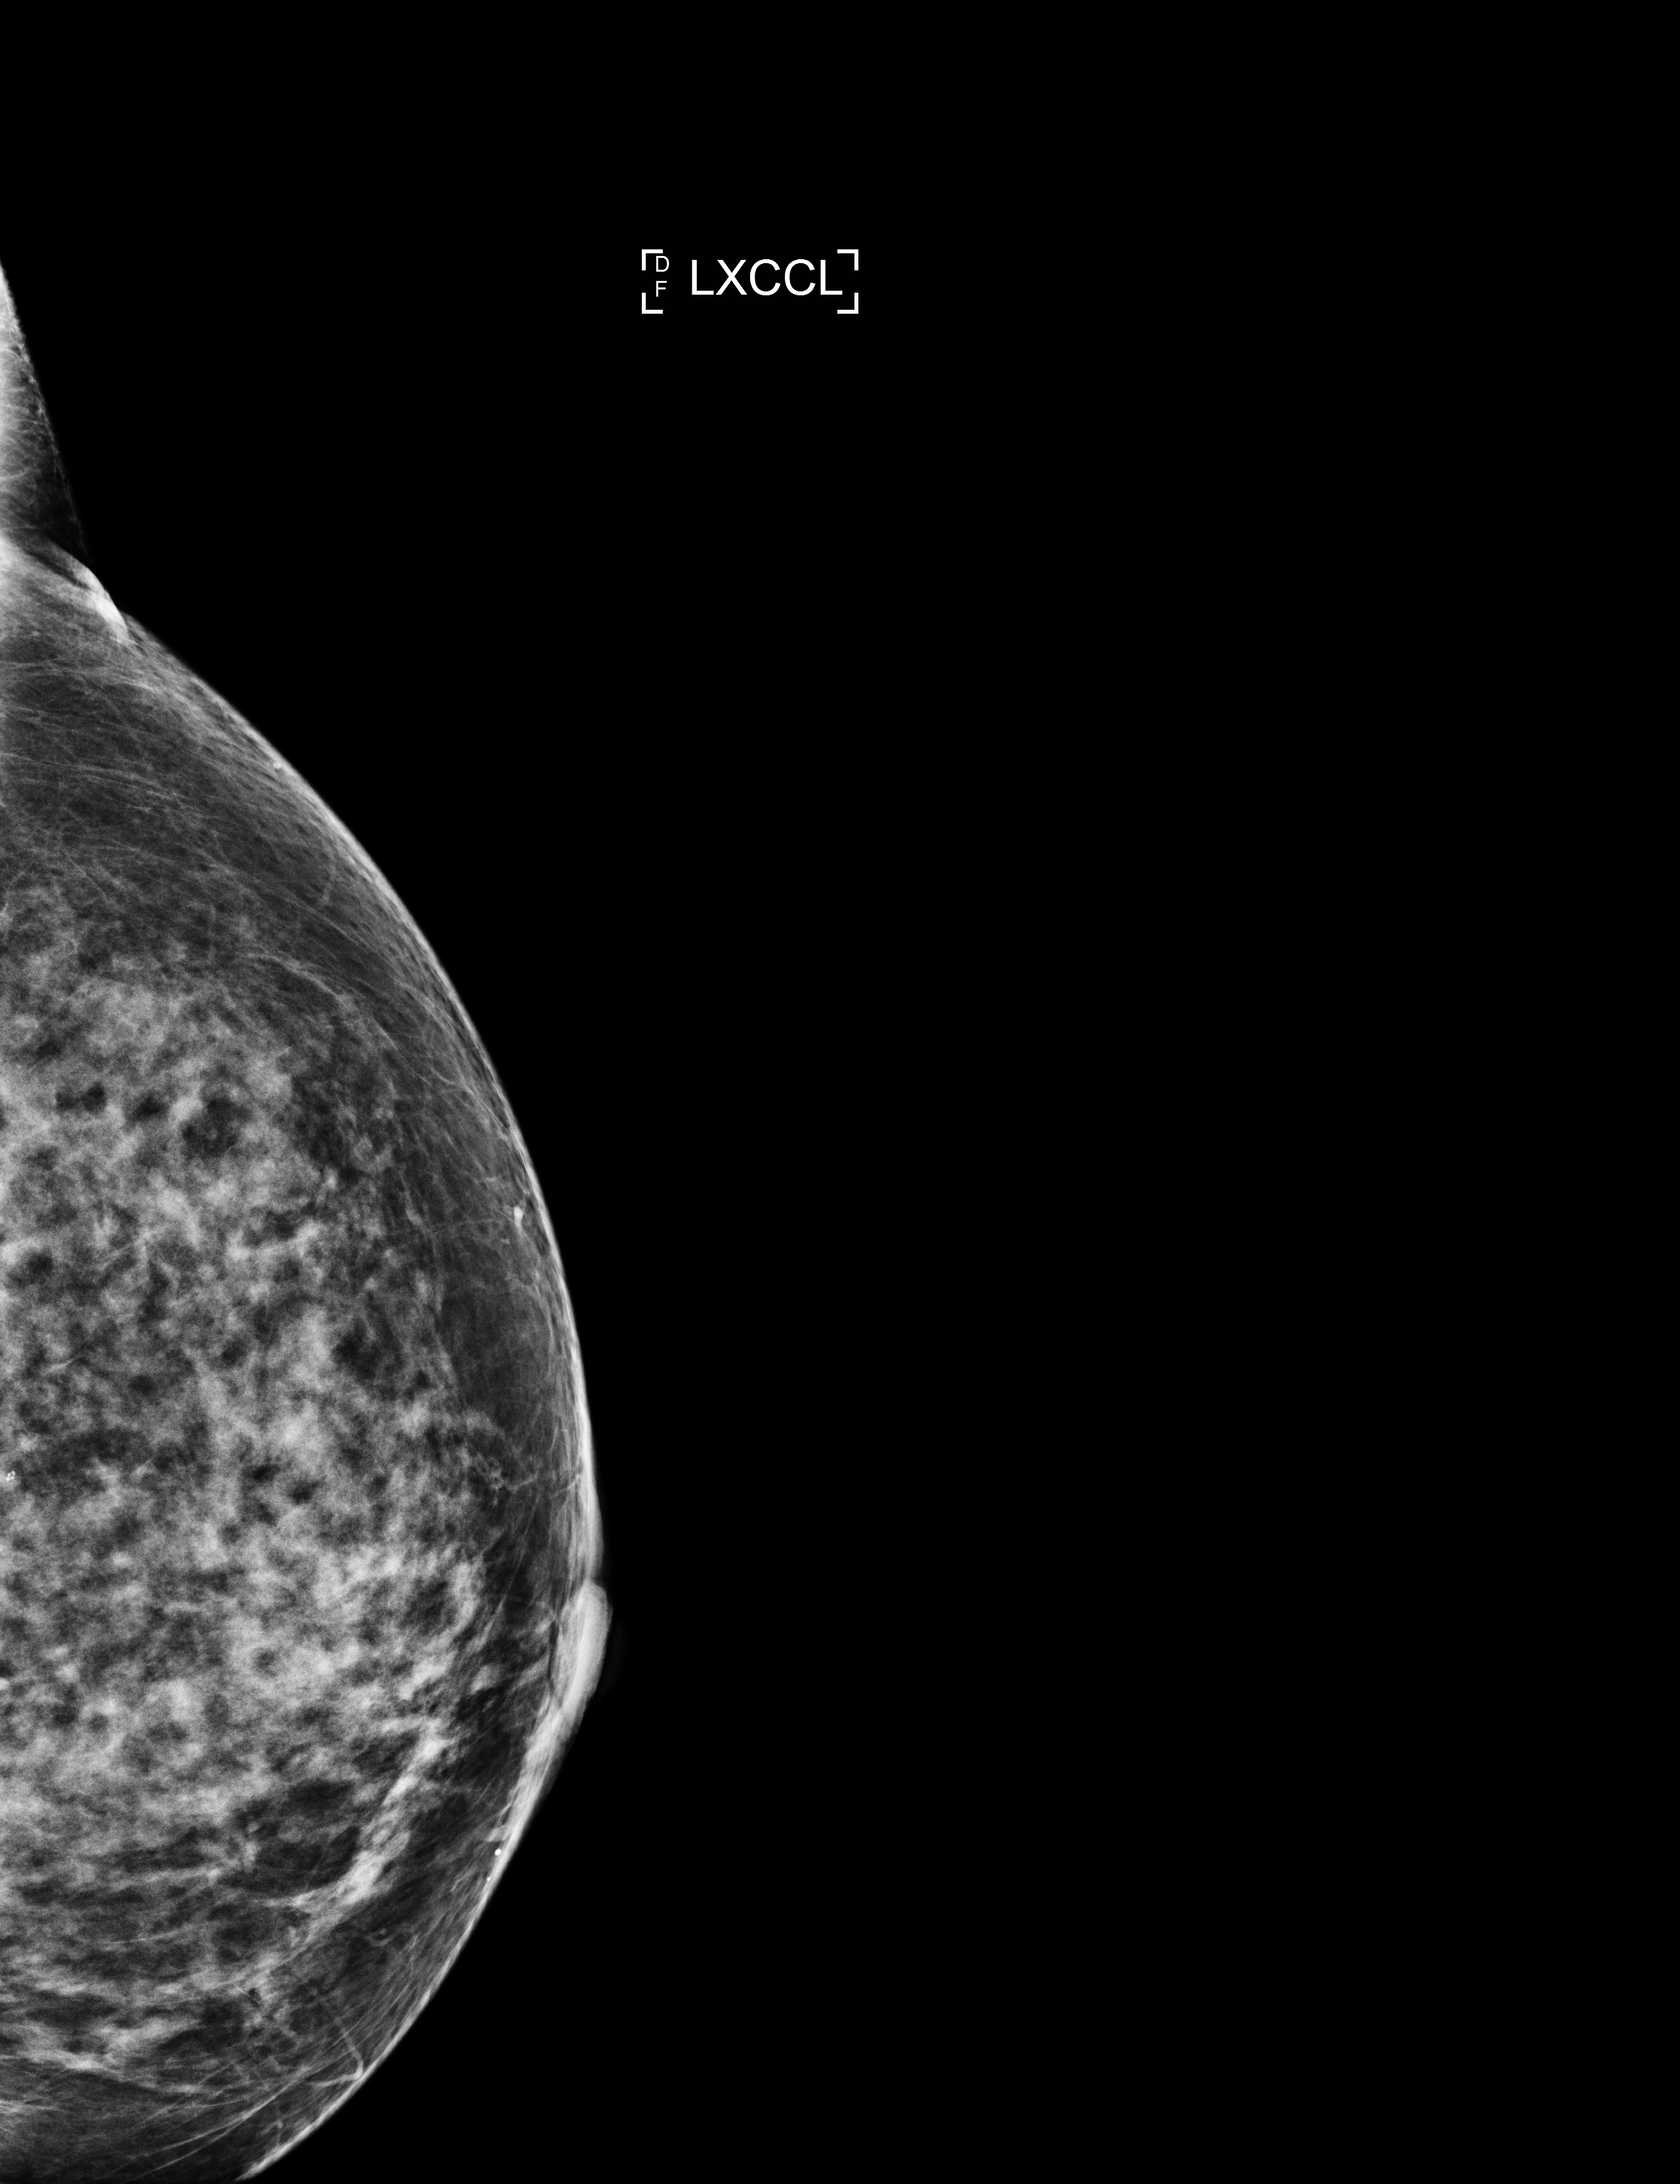
Full-field digital mammogram (FFDM), left breast, exaggerated CC view (lateral), screening examination. Patient: female, 65 years.
Breast density at the screening exam (both breasts): heterogeneously dense (BI-RADS density category c). Final BI-RADS category for the screening round (tomosynthesis exam, both breasts): category 1. Recall: no recall after this screen.